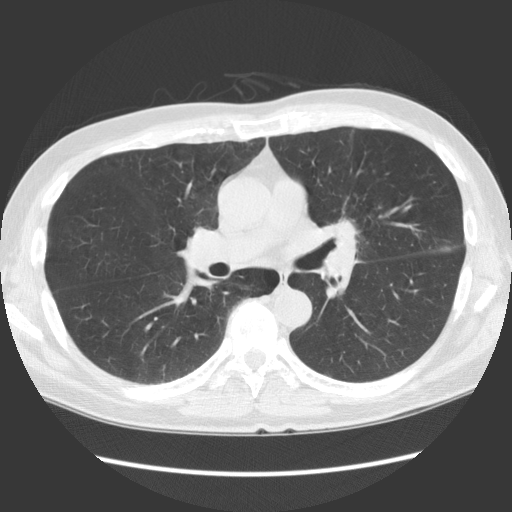
Axial slice from a low-dose chest CT screening exam. First (baseline) screen. Lung window (W 1500 / L -600 HU). 2.5 mm slice thickness. Male, age 61 years at enrolment. Former smoker at enrolment.
Expert-annotated lung lesion, box from (x=288, y=198) to (x=388, y=301) px. Screening reader's record for this exam (one nodule recorded; not confirmed to be the boxed lesion): non-calcified nodule or mass ≥4 mm, lingula, 35 × 35 mm, spiculated (stellate) margins, soft tissue attenuation. Official screen result: positive, change unspecified: nodule(s) >= 4 mm or enlarging nodule(s), mass(es), or other non-specific abnormalities suspicious for lung cancer. Later outcome: lung cancer diagnosed 58 days after this screen — squamous cell carcinoma, NOS, left hilum, left main stem bronchus, poorly differentiated (G3), stage IA (AJCC 6th edition), 40 mm at pathology.